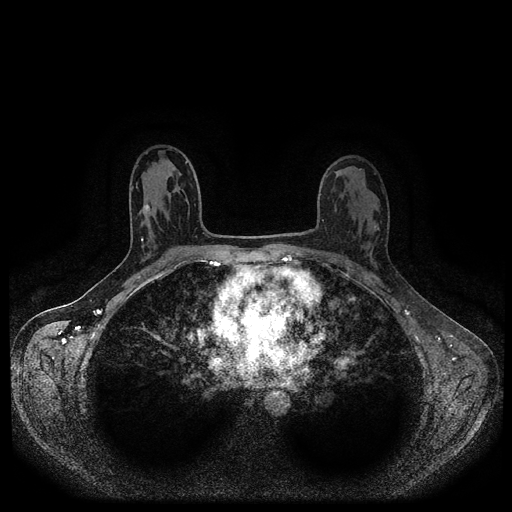
Breast MRI (dynamic contrast-enhanced, multi-phase), one axial slice; dynamic contrast-enhanced series, time point 2 of 5 at this slice position (early post-contrast); 1.5 T; TE 2.6 ms, TR 5.4 ms; 2 mm slice thickness; 512 × 512 image matrix. Patient: female, 30 years.
Structures marked on this image (semi-automatically segmented with operator editing):
- breast lesion (labelled benign in the annotation): box from (x=143, y=204) to (x=150, y=213) px